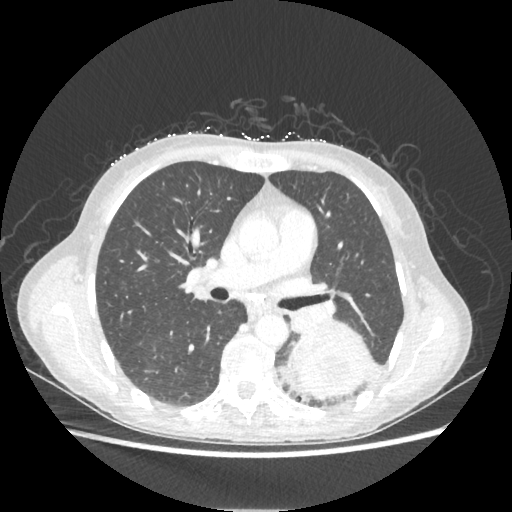
Chest CT, one axial slice; position 126 of 221 along the scan axis; 80 kVp; lung window (W 1500 / L -600 HU); 512 × 512 image matrix. Female patient, age 53 years. Case-level facts recorded for this patient, not image findings: clinical TNM (as recorded): T3 N0 M0.
Outlined on this slice (rectangle marked by the reading radiologist):
- lung tumour (recorded histology: adenocarcinoma): box from (x=293, y=321) to (x=371, y=401) px